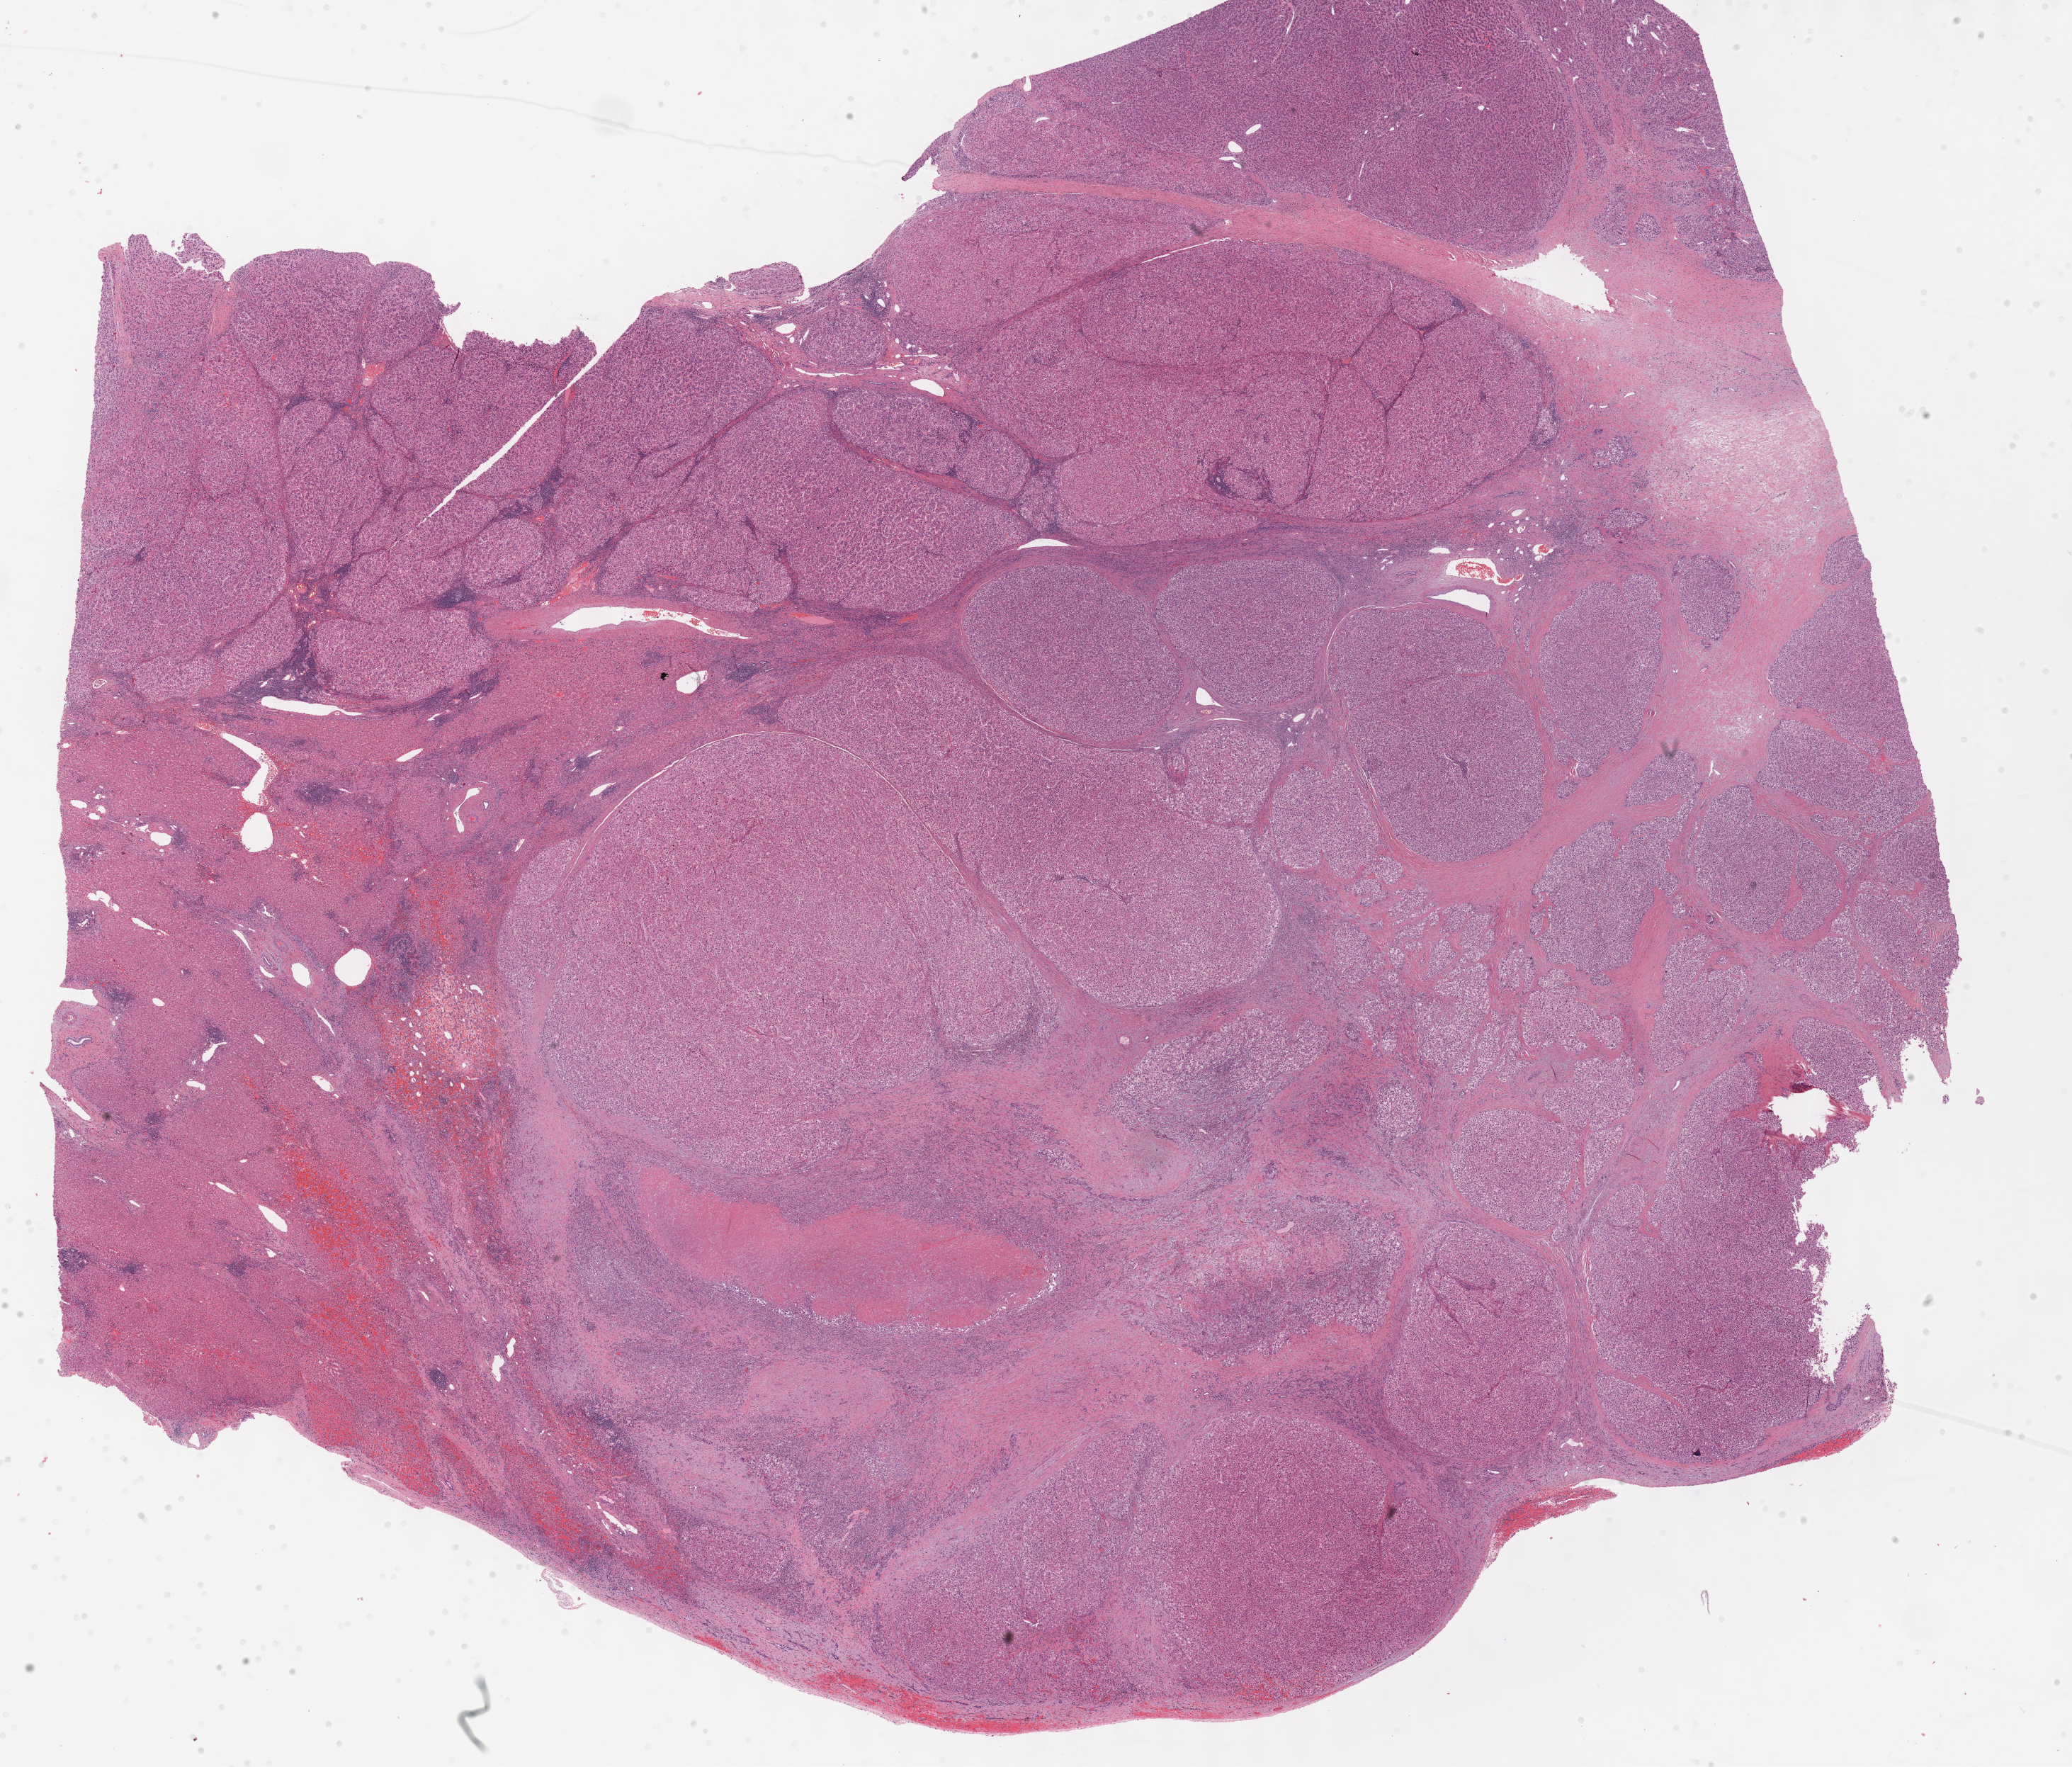
H&E-stained whole-slide image, shown as a low-resolution overview of the whole scanned area (about 23.6 x 20.2 mm, acquisition: 40x scan); formalin-fixed paraffin-embedded (FFPE) diagnostic section; liver, primary tumour sample. Male, age 53 years at initial diagnosis. Histologic grade: G2 (moderately differentiated).
Diagnosis: Hepatocellular carcinoma, NOS. AJCC pathologic stage: IIIA (7th edition).